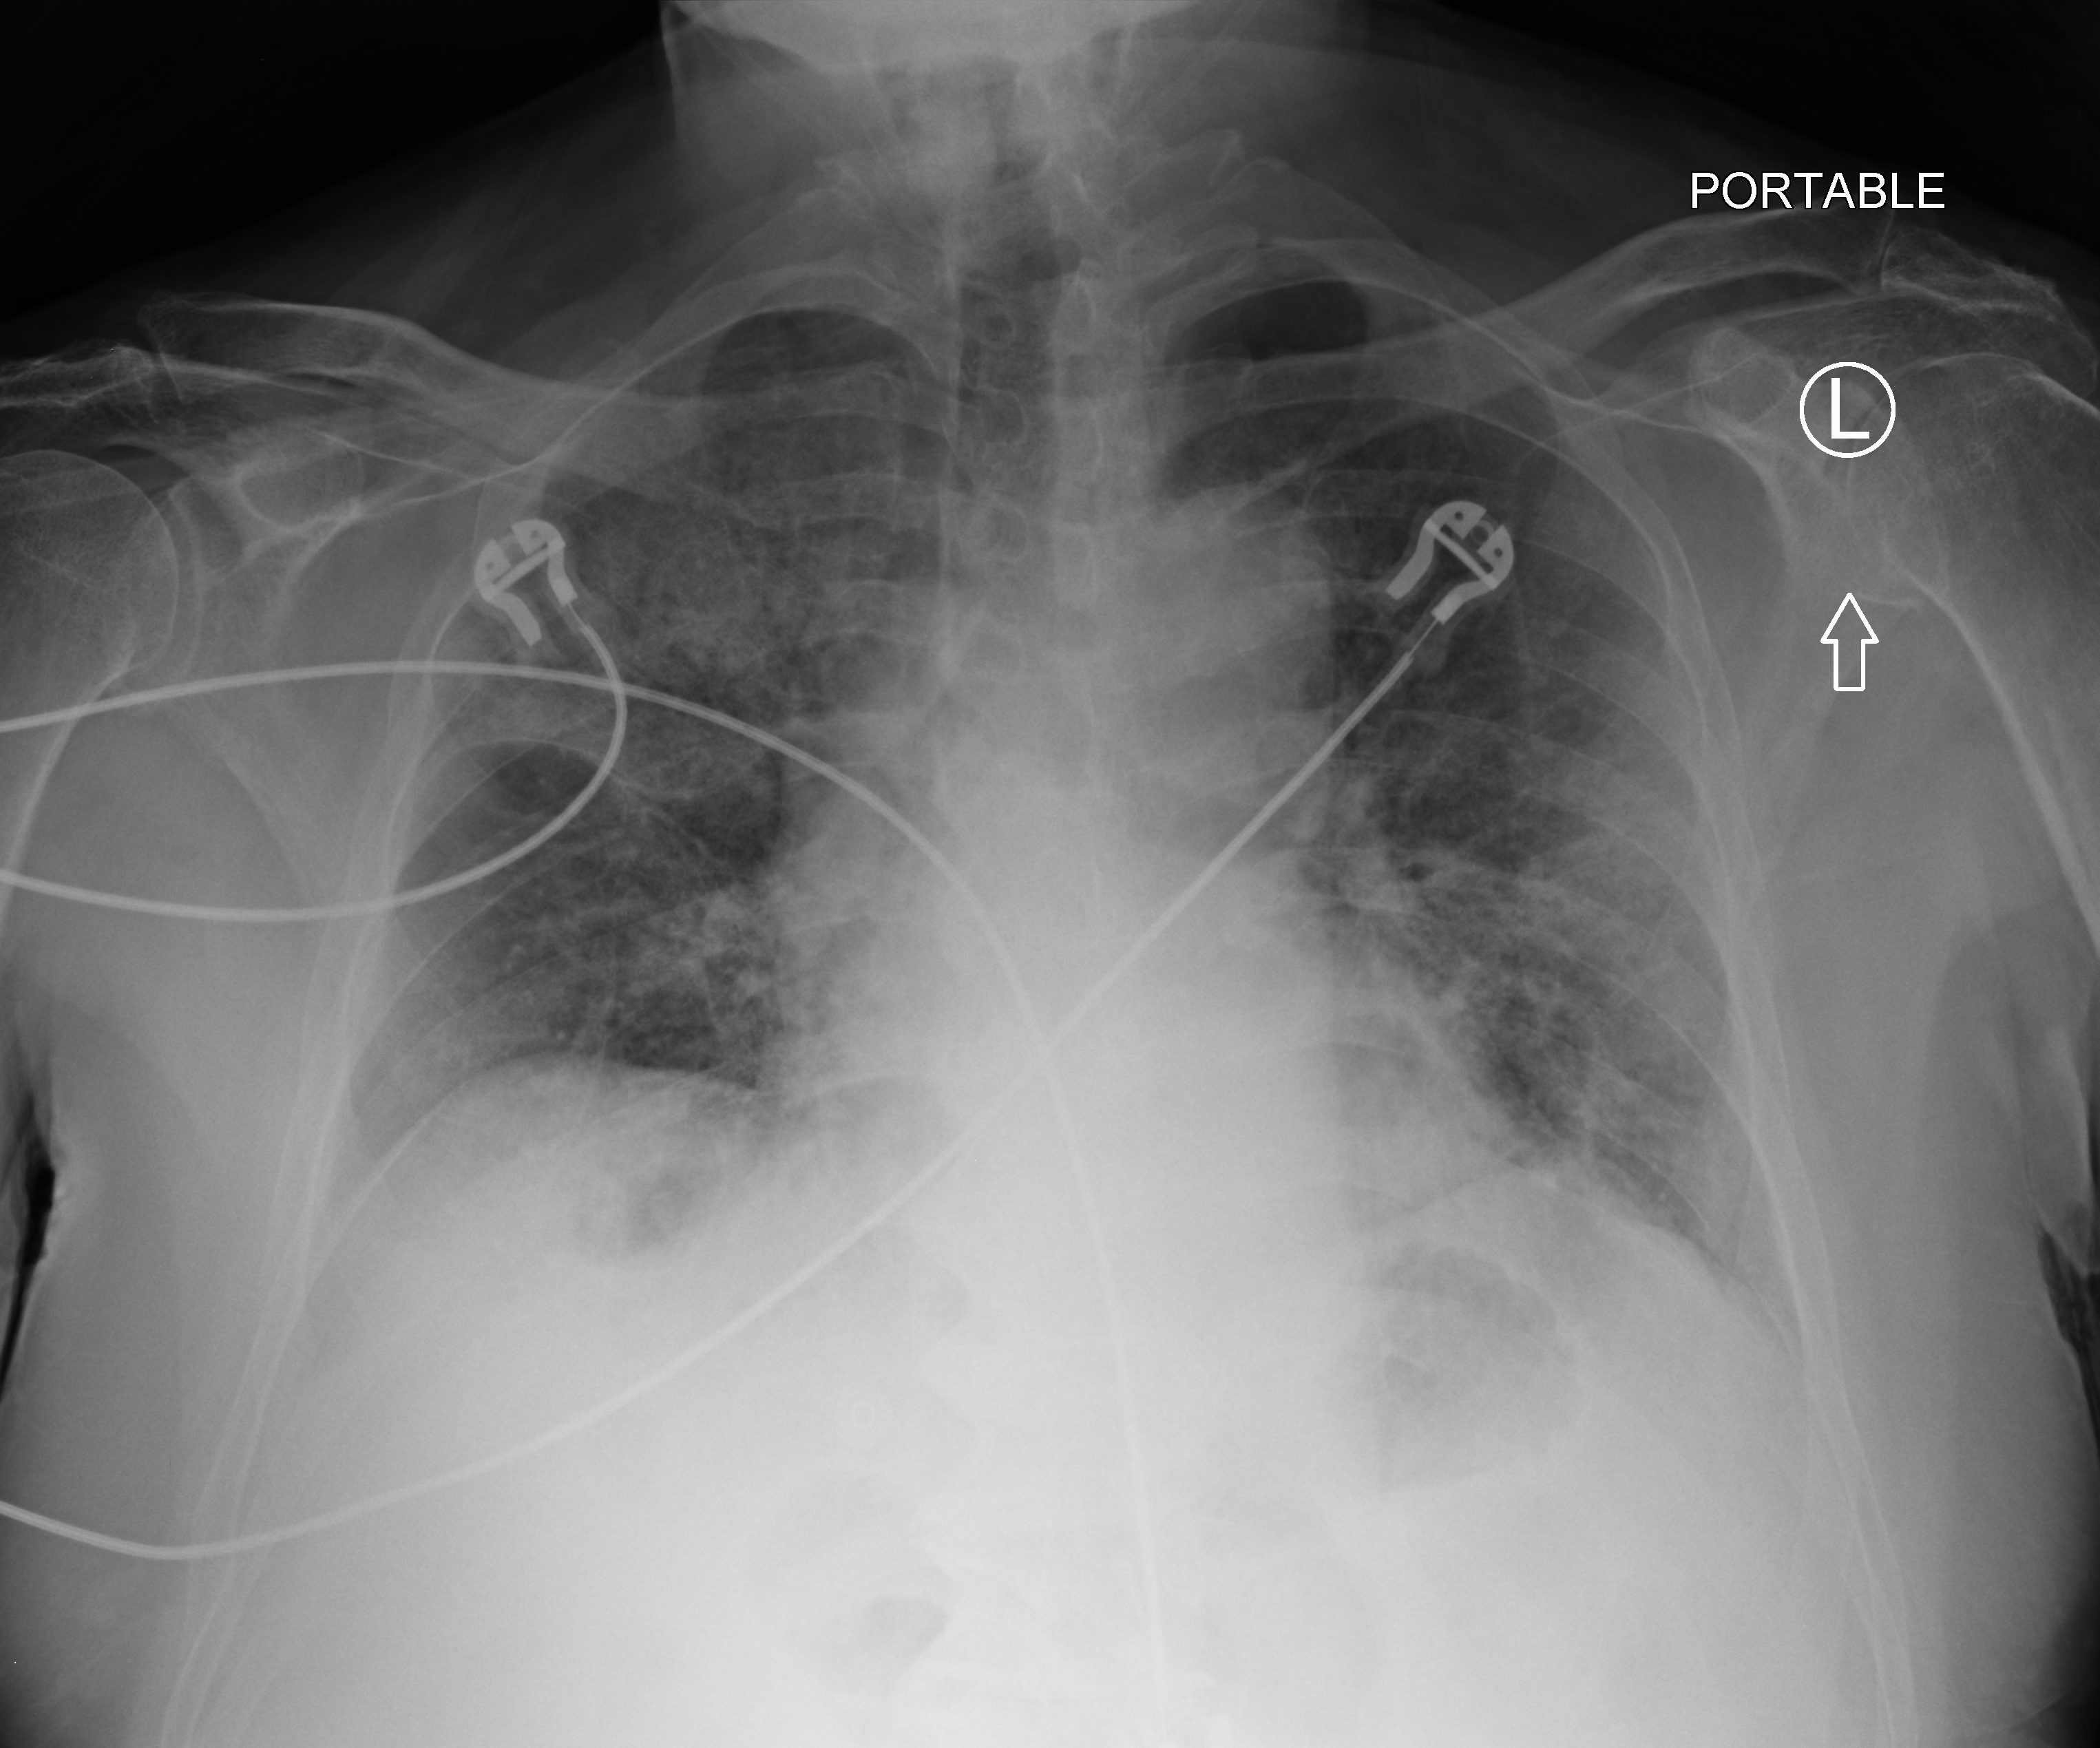
Chest X-ray (portable), anteroposterior (AP) projection. Male patient hospitalised with COVID-19, age 75–90 years.
From the hospital-stay record, not from the radiograph (when in the stay this image was taken is not recorded): admitted to intensive care during this hospital stay: no.